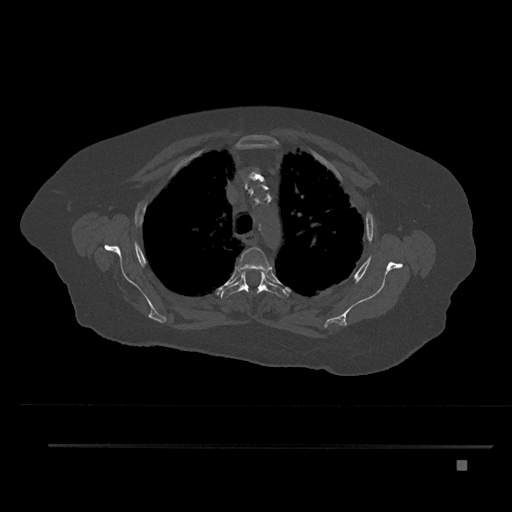
CT including the spine, one axial slice. Slice 615 of 797 in the series (ordered by position). 120 kVp. Bone window (W 1800 / L 400 HU). 0.5 mm slice thickness. 512 × 512 image matrix. Patient: female, 76 years. From the clinical record (not read from this slice): primary cancer: lung; vertebrae with lytic lesions (as recorded): T11, L3.
Structures marked on this image (semi-automatically segmented with operator editing):
- T3 vertebra: box from (x=237, y=247) to (x=271, y=291) px
- T4 vertebra: (x=220, y=268)–(x=289, y=299)